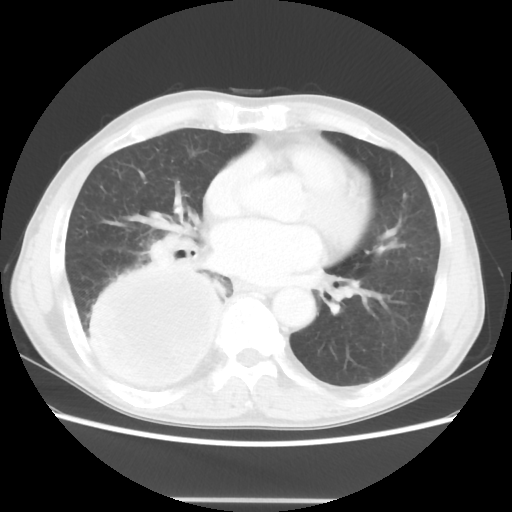
Chest CT, one axial slice. Slice 20 of 48 in the series (ordered by position). Reconstruction kernel STANDARD. 100 kVp. Lung window (W 1500 / L -600 HU). 5 mm slice thickness. 512 × 512 image matrix, field of view 361 × 361 mm. Male patient, age 66 years. Case-level facts recorded for this patient, not image findings: clinical TNM (as recorded): T4 N1 M1.
Annotated regions visible in this slice (rectangle marked by the reading radiologist):
- lung tumour (recorded histology: small cell carcinoma): box from (x=69, y=256) to (x=222, y=394) px